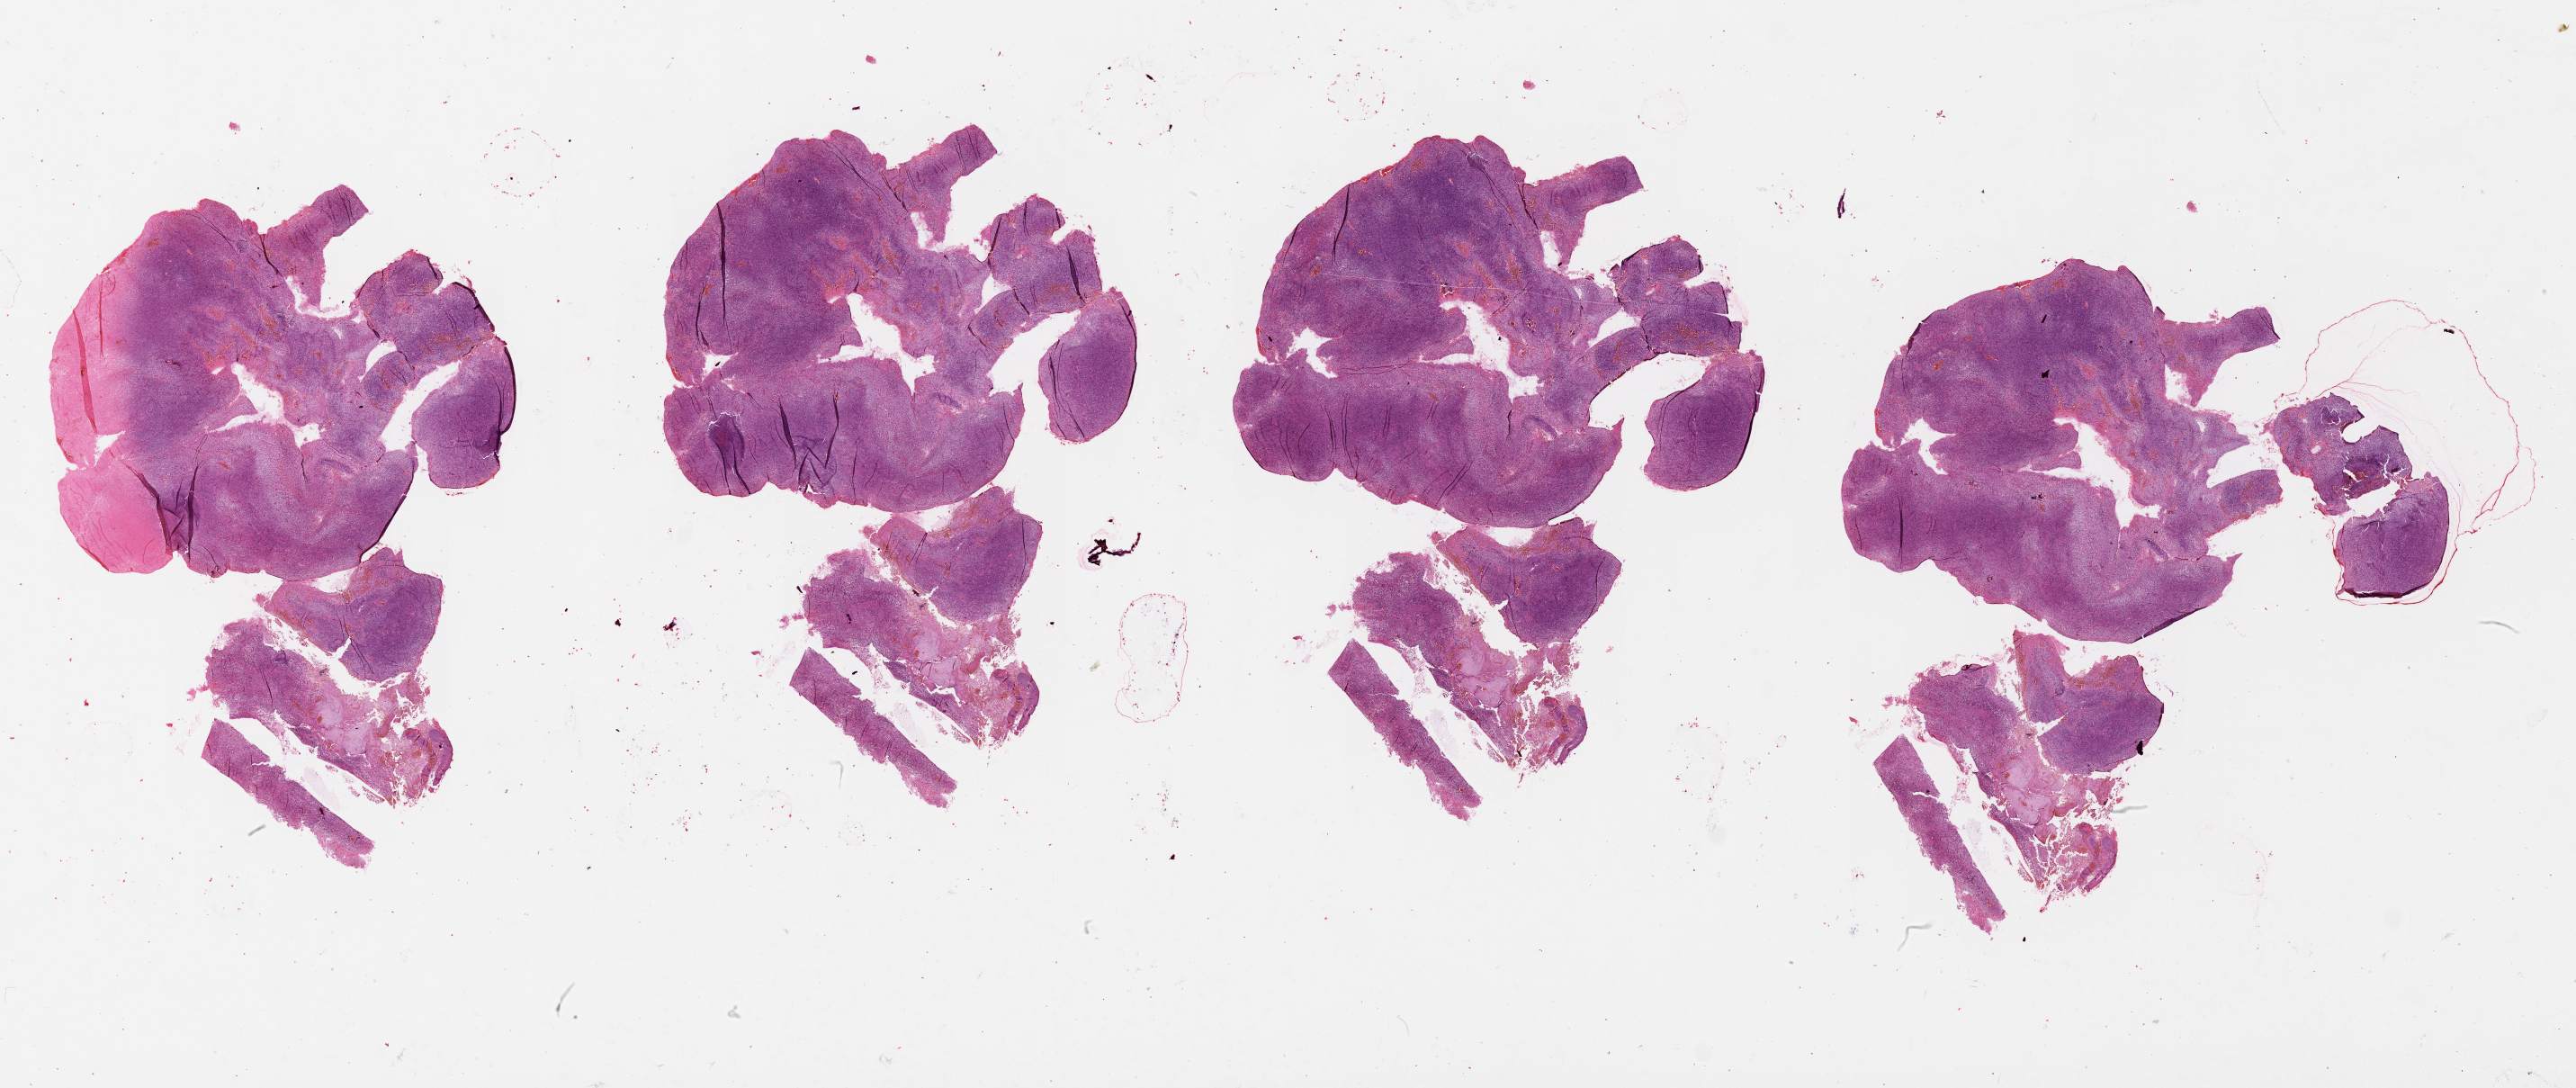
Whole-slide histology image, Hematoxylin and eosin (H&E) stained, shown as a low-resolution overview of the whole scanned area (about 46.1 x 19.5 mm, slide scanned at 20x). Tumour tissue sample, brain. Female, 37 y/o.
Histologic diagnosis: Glioblastoma. Primary tumour site (as recorded): occipital lobe.